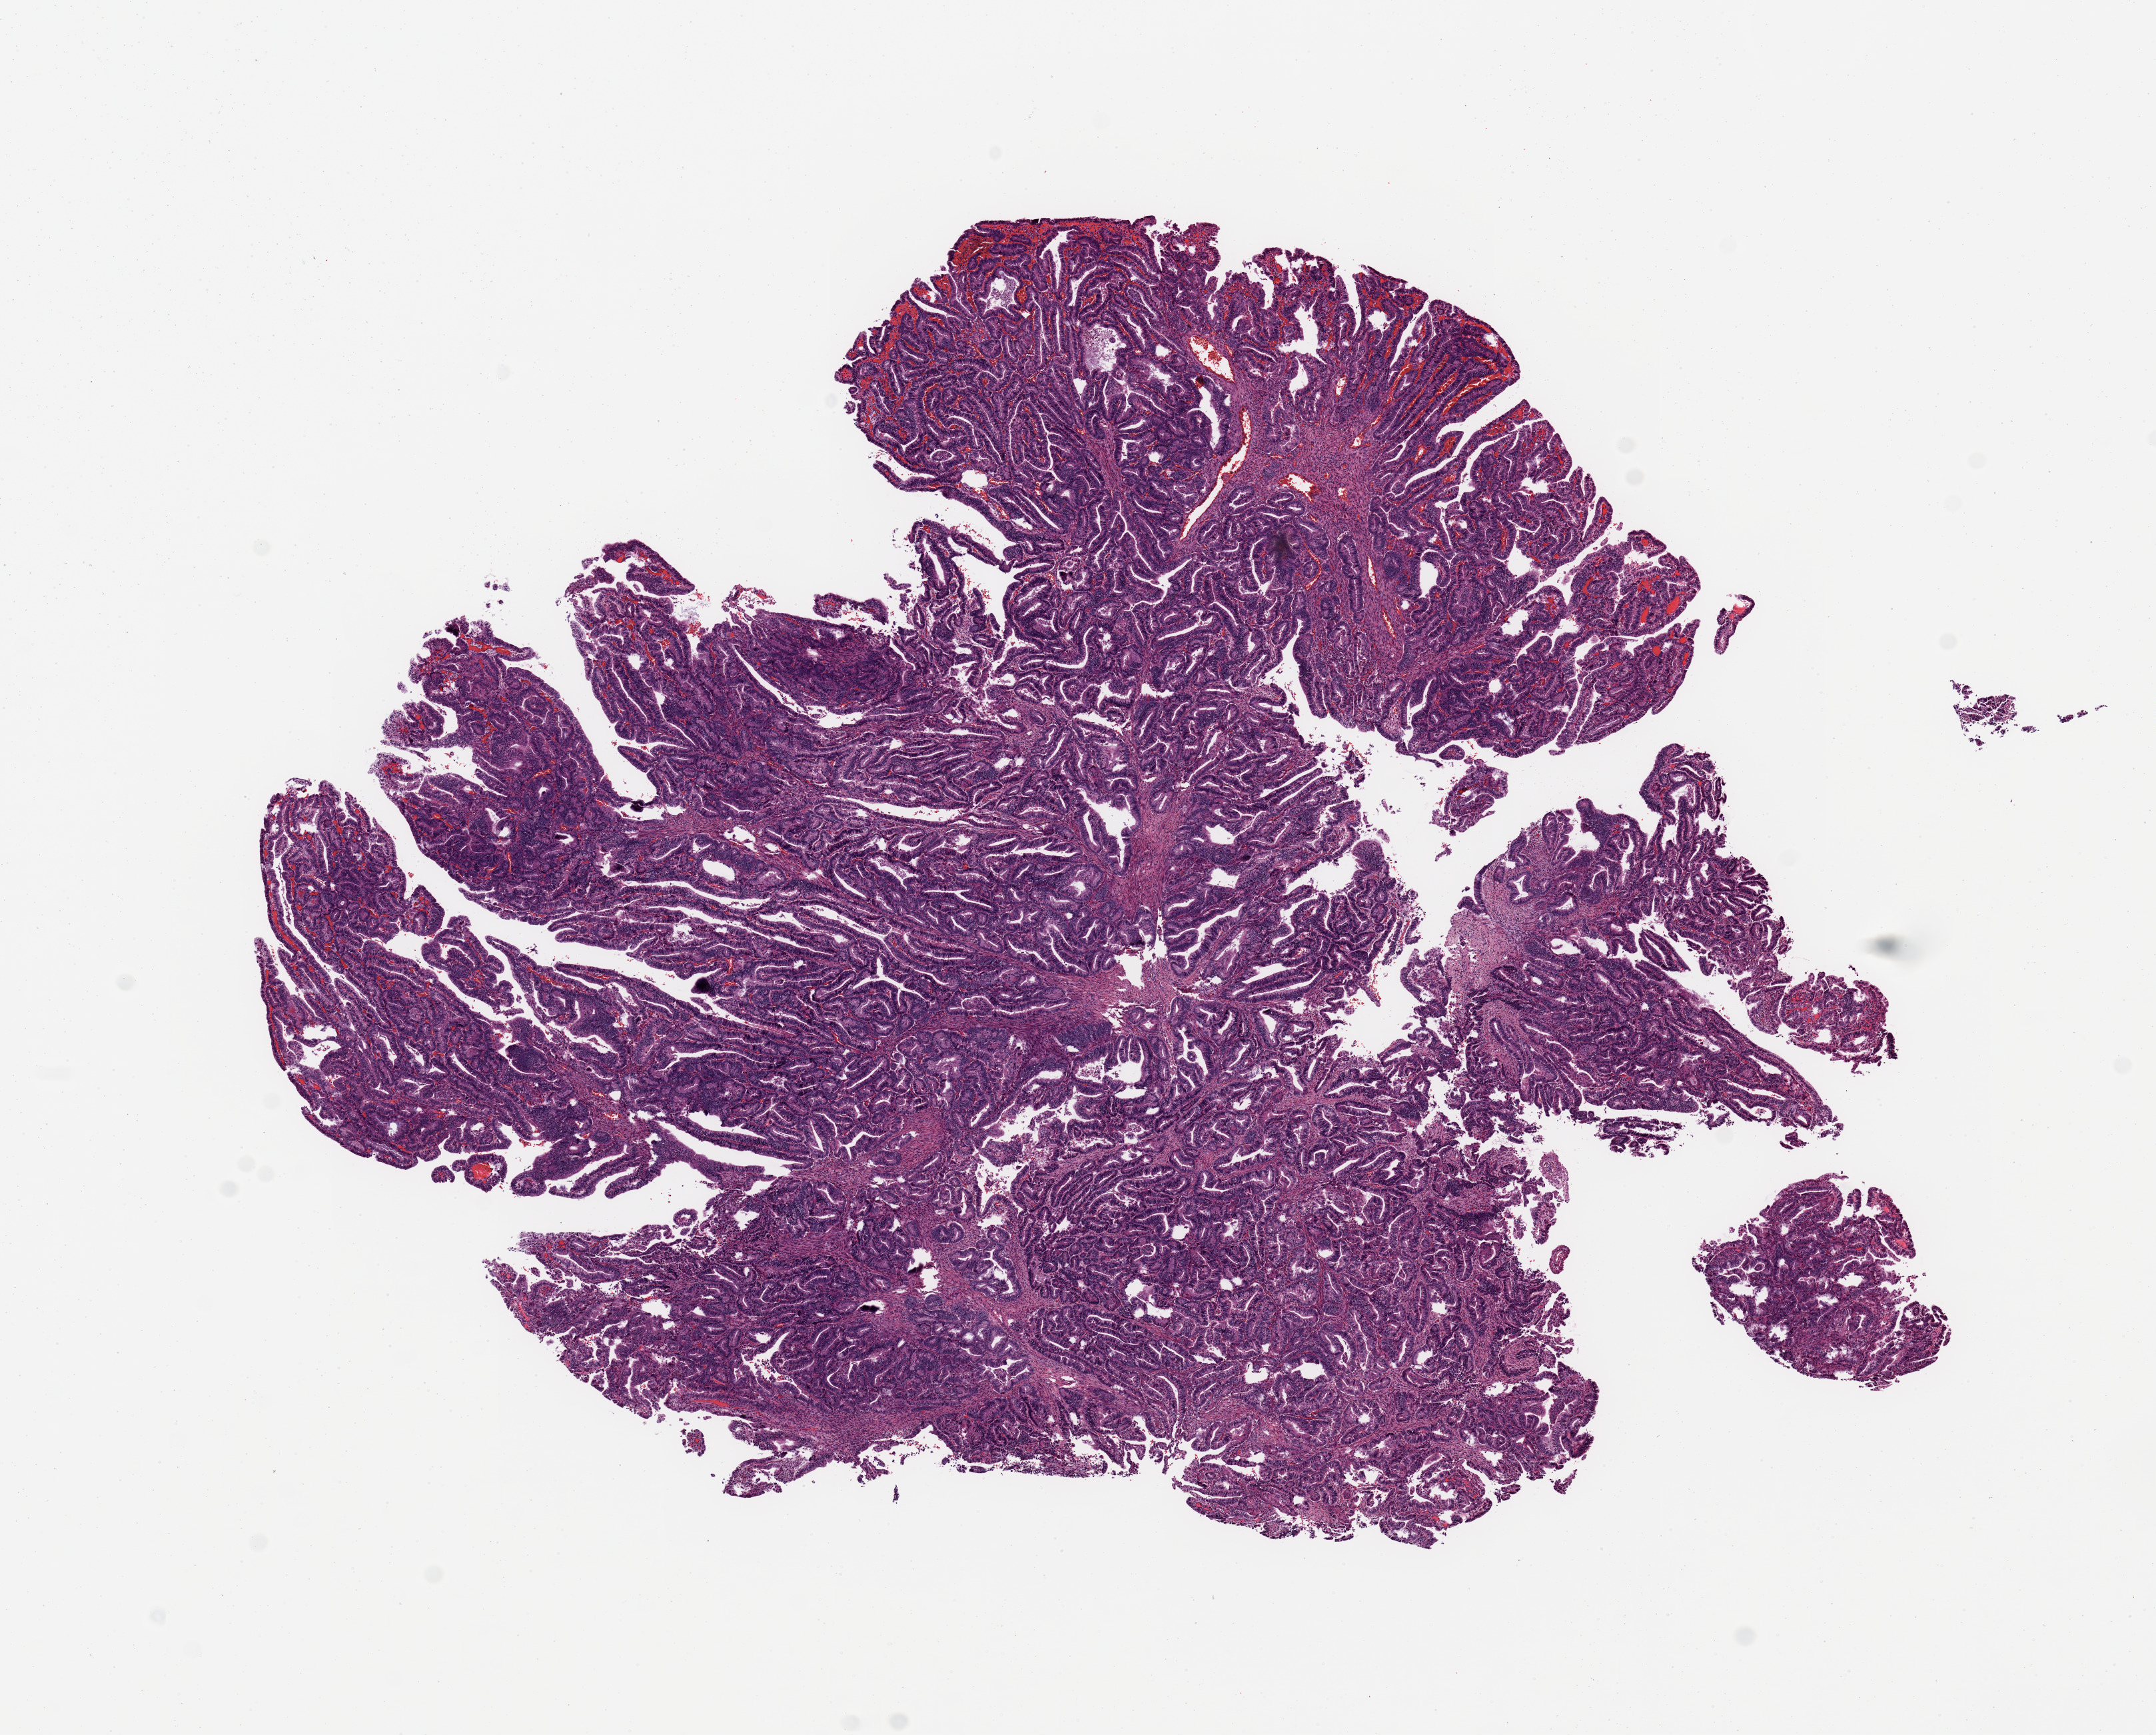
Whole-slide histology image, H&E, shown as a low-resolution overview of the whole scanned area (about 12.8 x 10.3 mm). Tumour tissue sample, uterus. Female, 38 y/o.
Histologic diagnosis: Endometrioid adenocarcinoma, NOS.